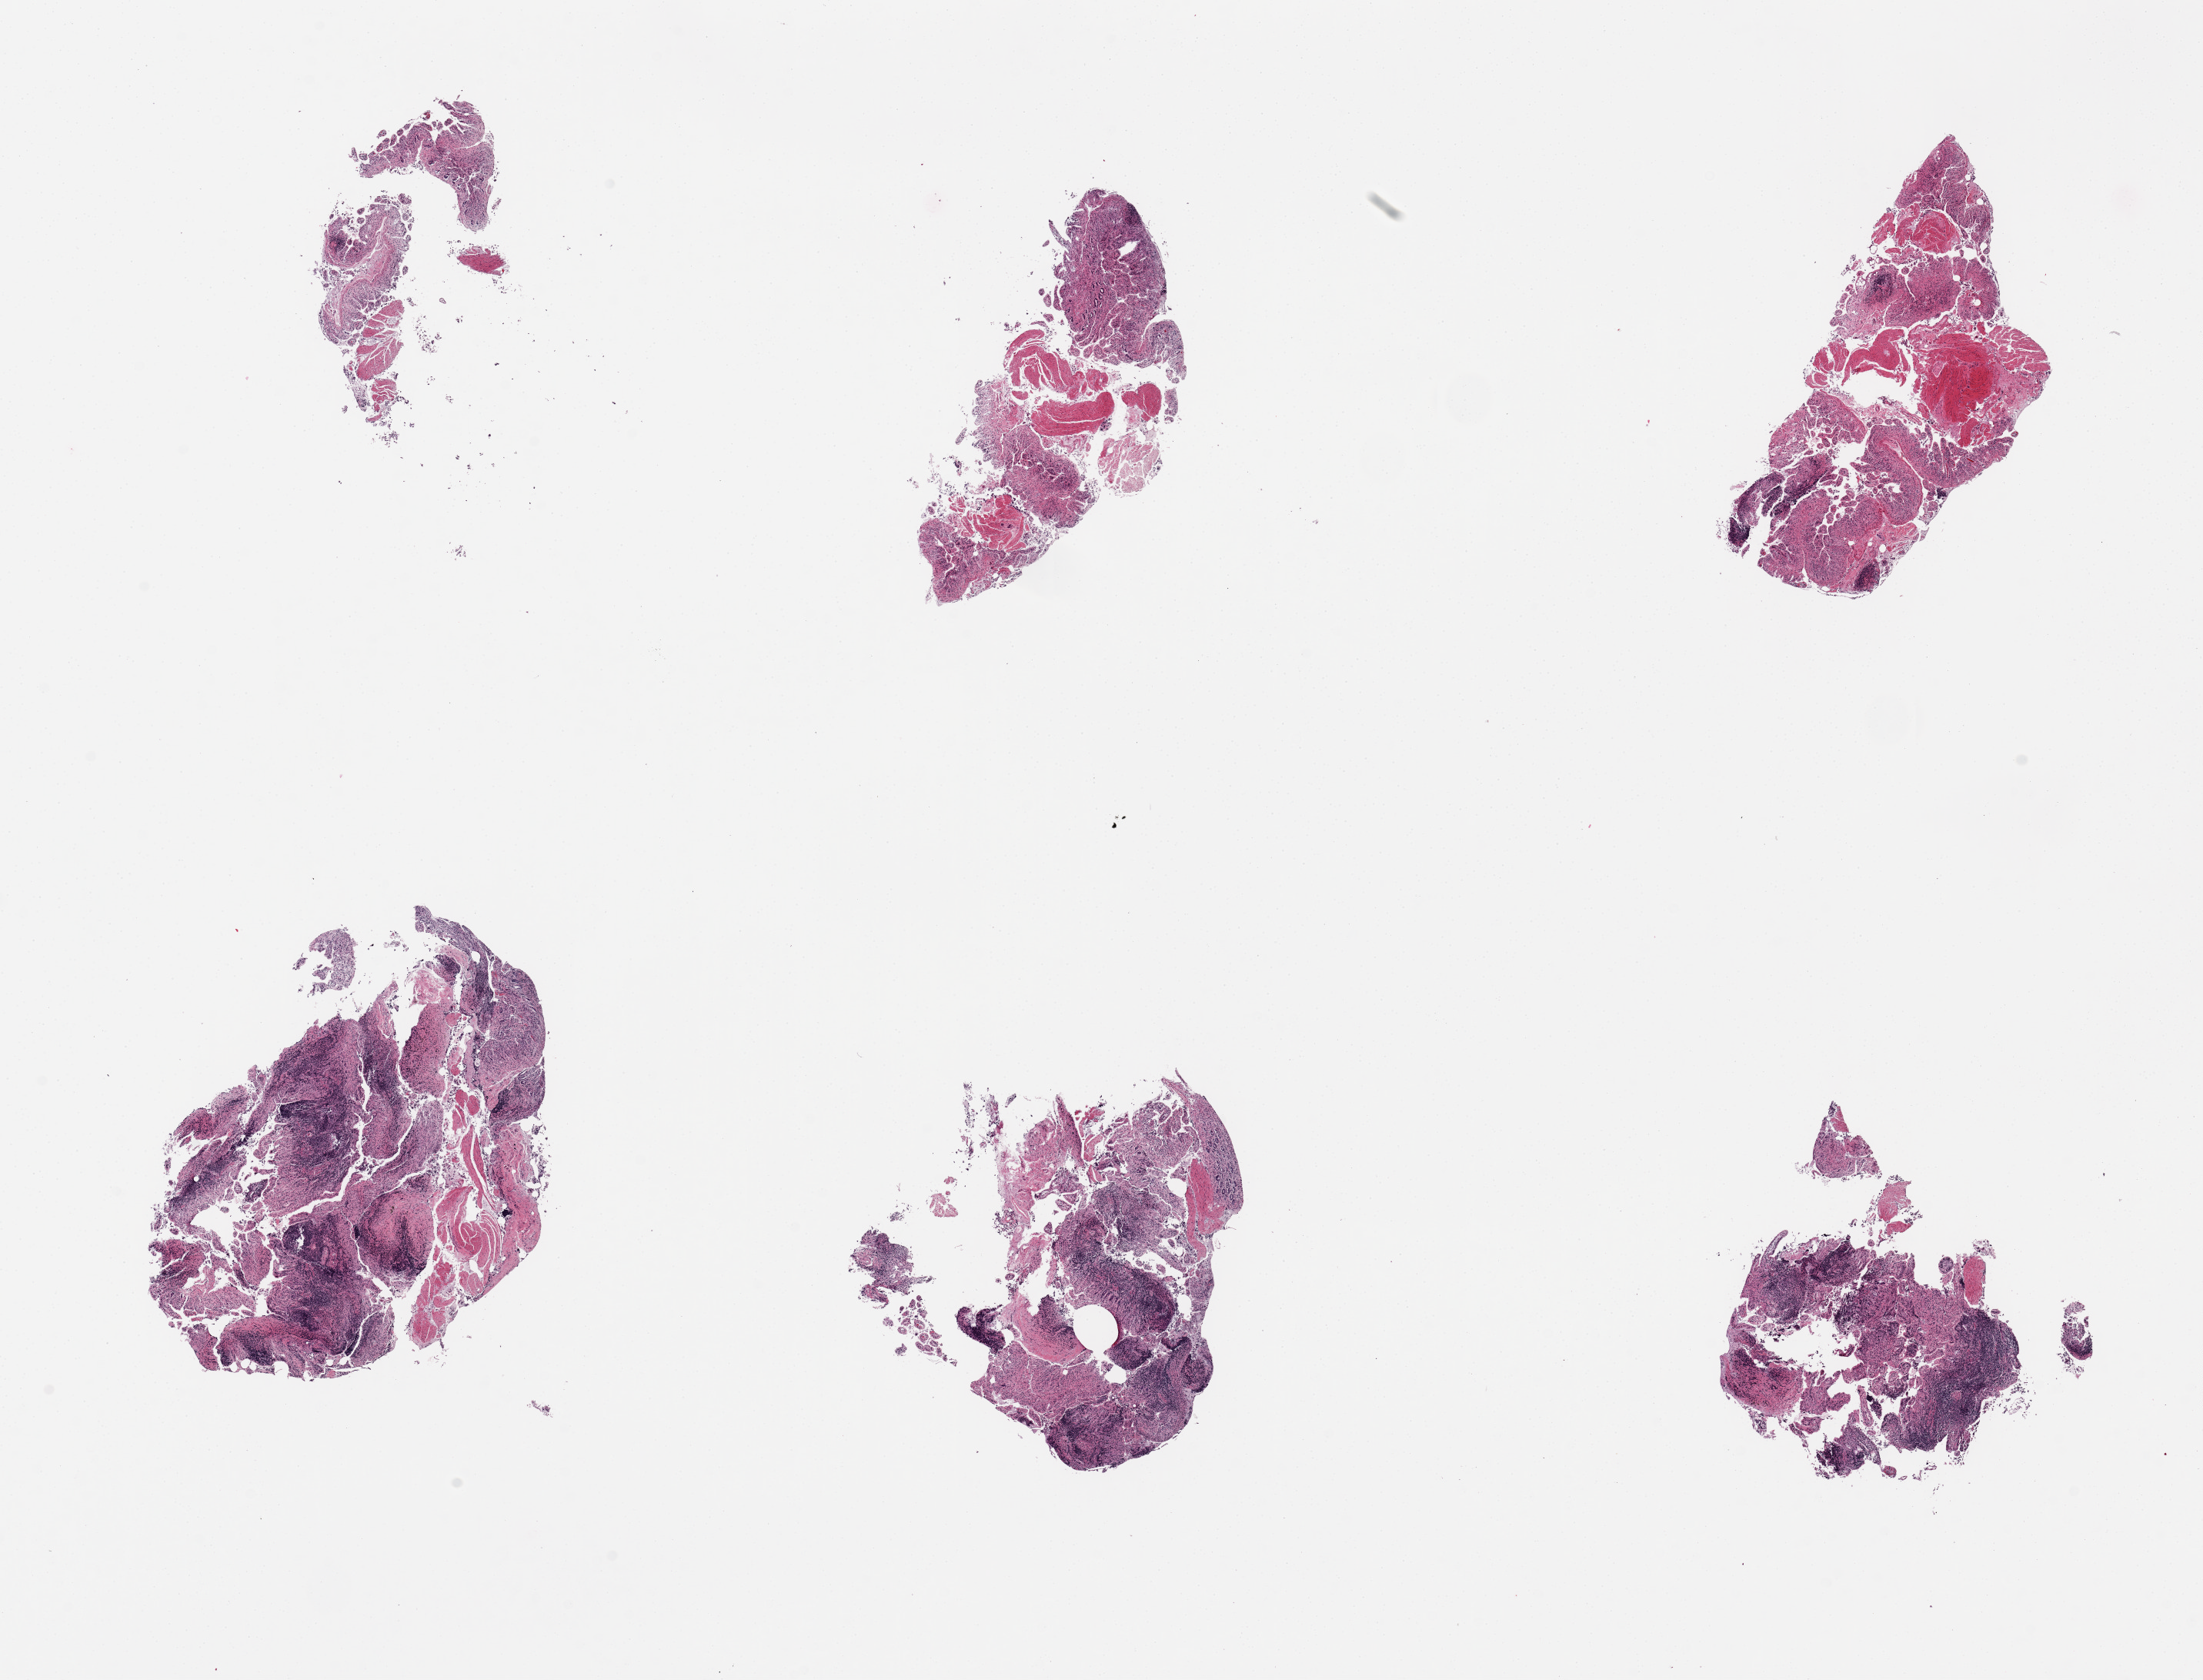
Digitized hematoxylin and eosin (H&E)-stained section, brightfield — shown as a low-resolution overview of the whole scanned area (about 22.6 x 17.3 mm), PAXgene-fixed paraffin-embedded (PFPE) section, sampled site (target tissue): ileum, tissue donor sample. Donor sex: male.
Pathologist's review note for this sample: 6 pieces; 3 have lymphoid tissue but poorly defined and autolyzed.